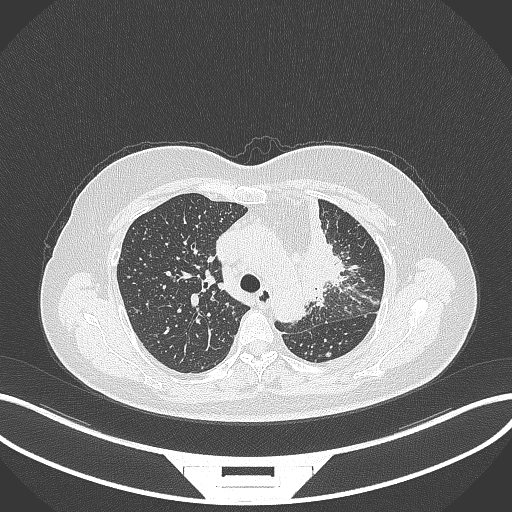
Chest CT, one axial slice; slice 237 of 348 in the series (ordered by position); reconstruction kernel B70f; lung window (W 1500 / L -600 HU); 1 mm slice thickness; 512 × 512 image matrix, field of view 400 × 400 mm. Female patient, age 49 years. Case-level facts recorded for this patient, not image findings: clinical TNM (as recorded): T1c N0 M1.
Outlined on this slice (rectangle marked by the reading radiologist):
- lung tumour (recorded histology: adenocarcinoma): box from (x=290, y=195) to (x=347, y=306) px